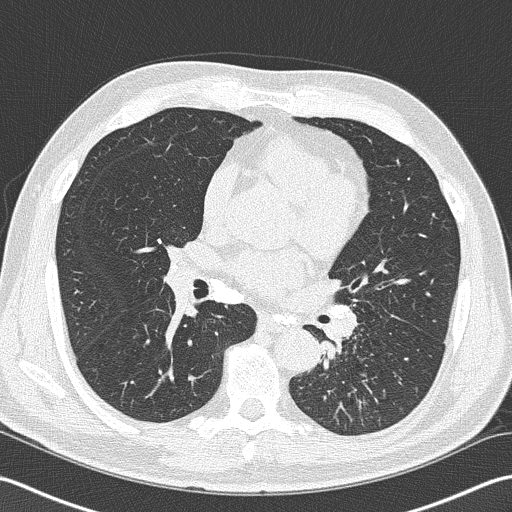
Low-dose screening chest CT, axial slice, second screening round (one year after baseline), lung window (W 1500 / L -600 HU), 2 mm slice thickness, lung (sharp) reconstruction kernel (B50f), 512 × 512 image matrix, field of view 350 × 350 mm. Male participant, aged 57 years at enrolment. Former smoker at enrolment.
Lesion marked by an expert reader, box from (x=292, y=296) to (x=373, y=380) px. Screening reader's record for this exam (one nodule recorded; not confirmed to be the boxed lesion): non-calcified nodule or mass ≥4 mm, left lower lobe, 40 × 30 mm, spiculated (stellate) margins, soft tissue attenuation, pre-existing on the prior screen: no. Later outcome: lung cancer diagnosed 9 days after this screen — squamous cell carcinoma, NOS, left lower lobe, moderately differentiated (G2), stage IIIB (AJCC 6th edition), 38 mm at pathology.